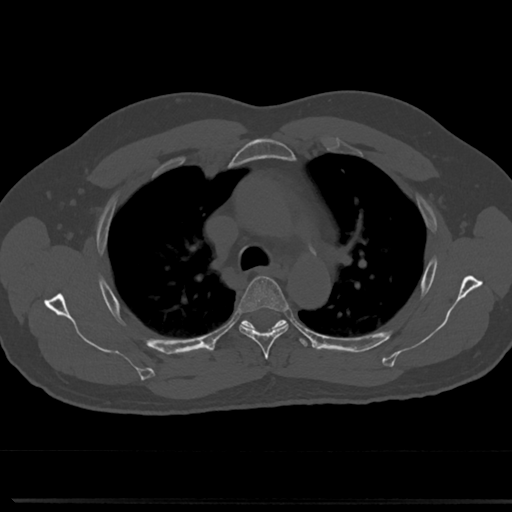
CT including the spine, one axial slice. Position 532 of 817 along the scan axis. Reconstruction kernel Br40s/3. Bone window (W 1800 / L 400 HU). 0.5 mm slice thickness. 512 × 512 image matrix. Male patient, age 61 years. Case-level facts recorded for this patient, not image findings: primary cancer: prostate.
Structures marked on this image (semi-automatically segmented with operator editing):
- T4 vertebra: box from (x=238, y=276) to (x=290, y=356) px
- T5 vertebra: (x=244, y=320)–(x=284, y=327)